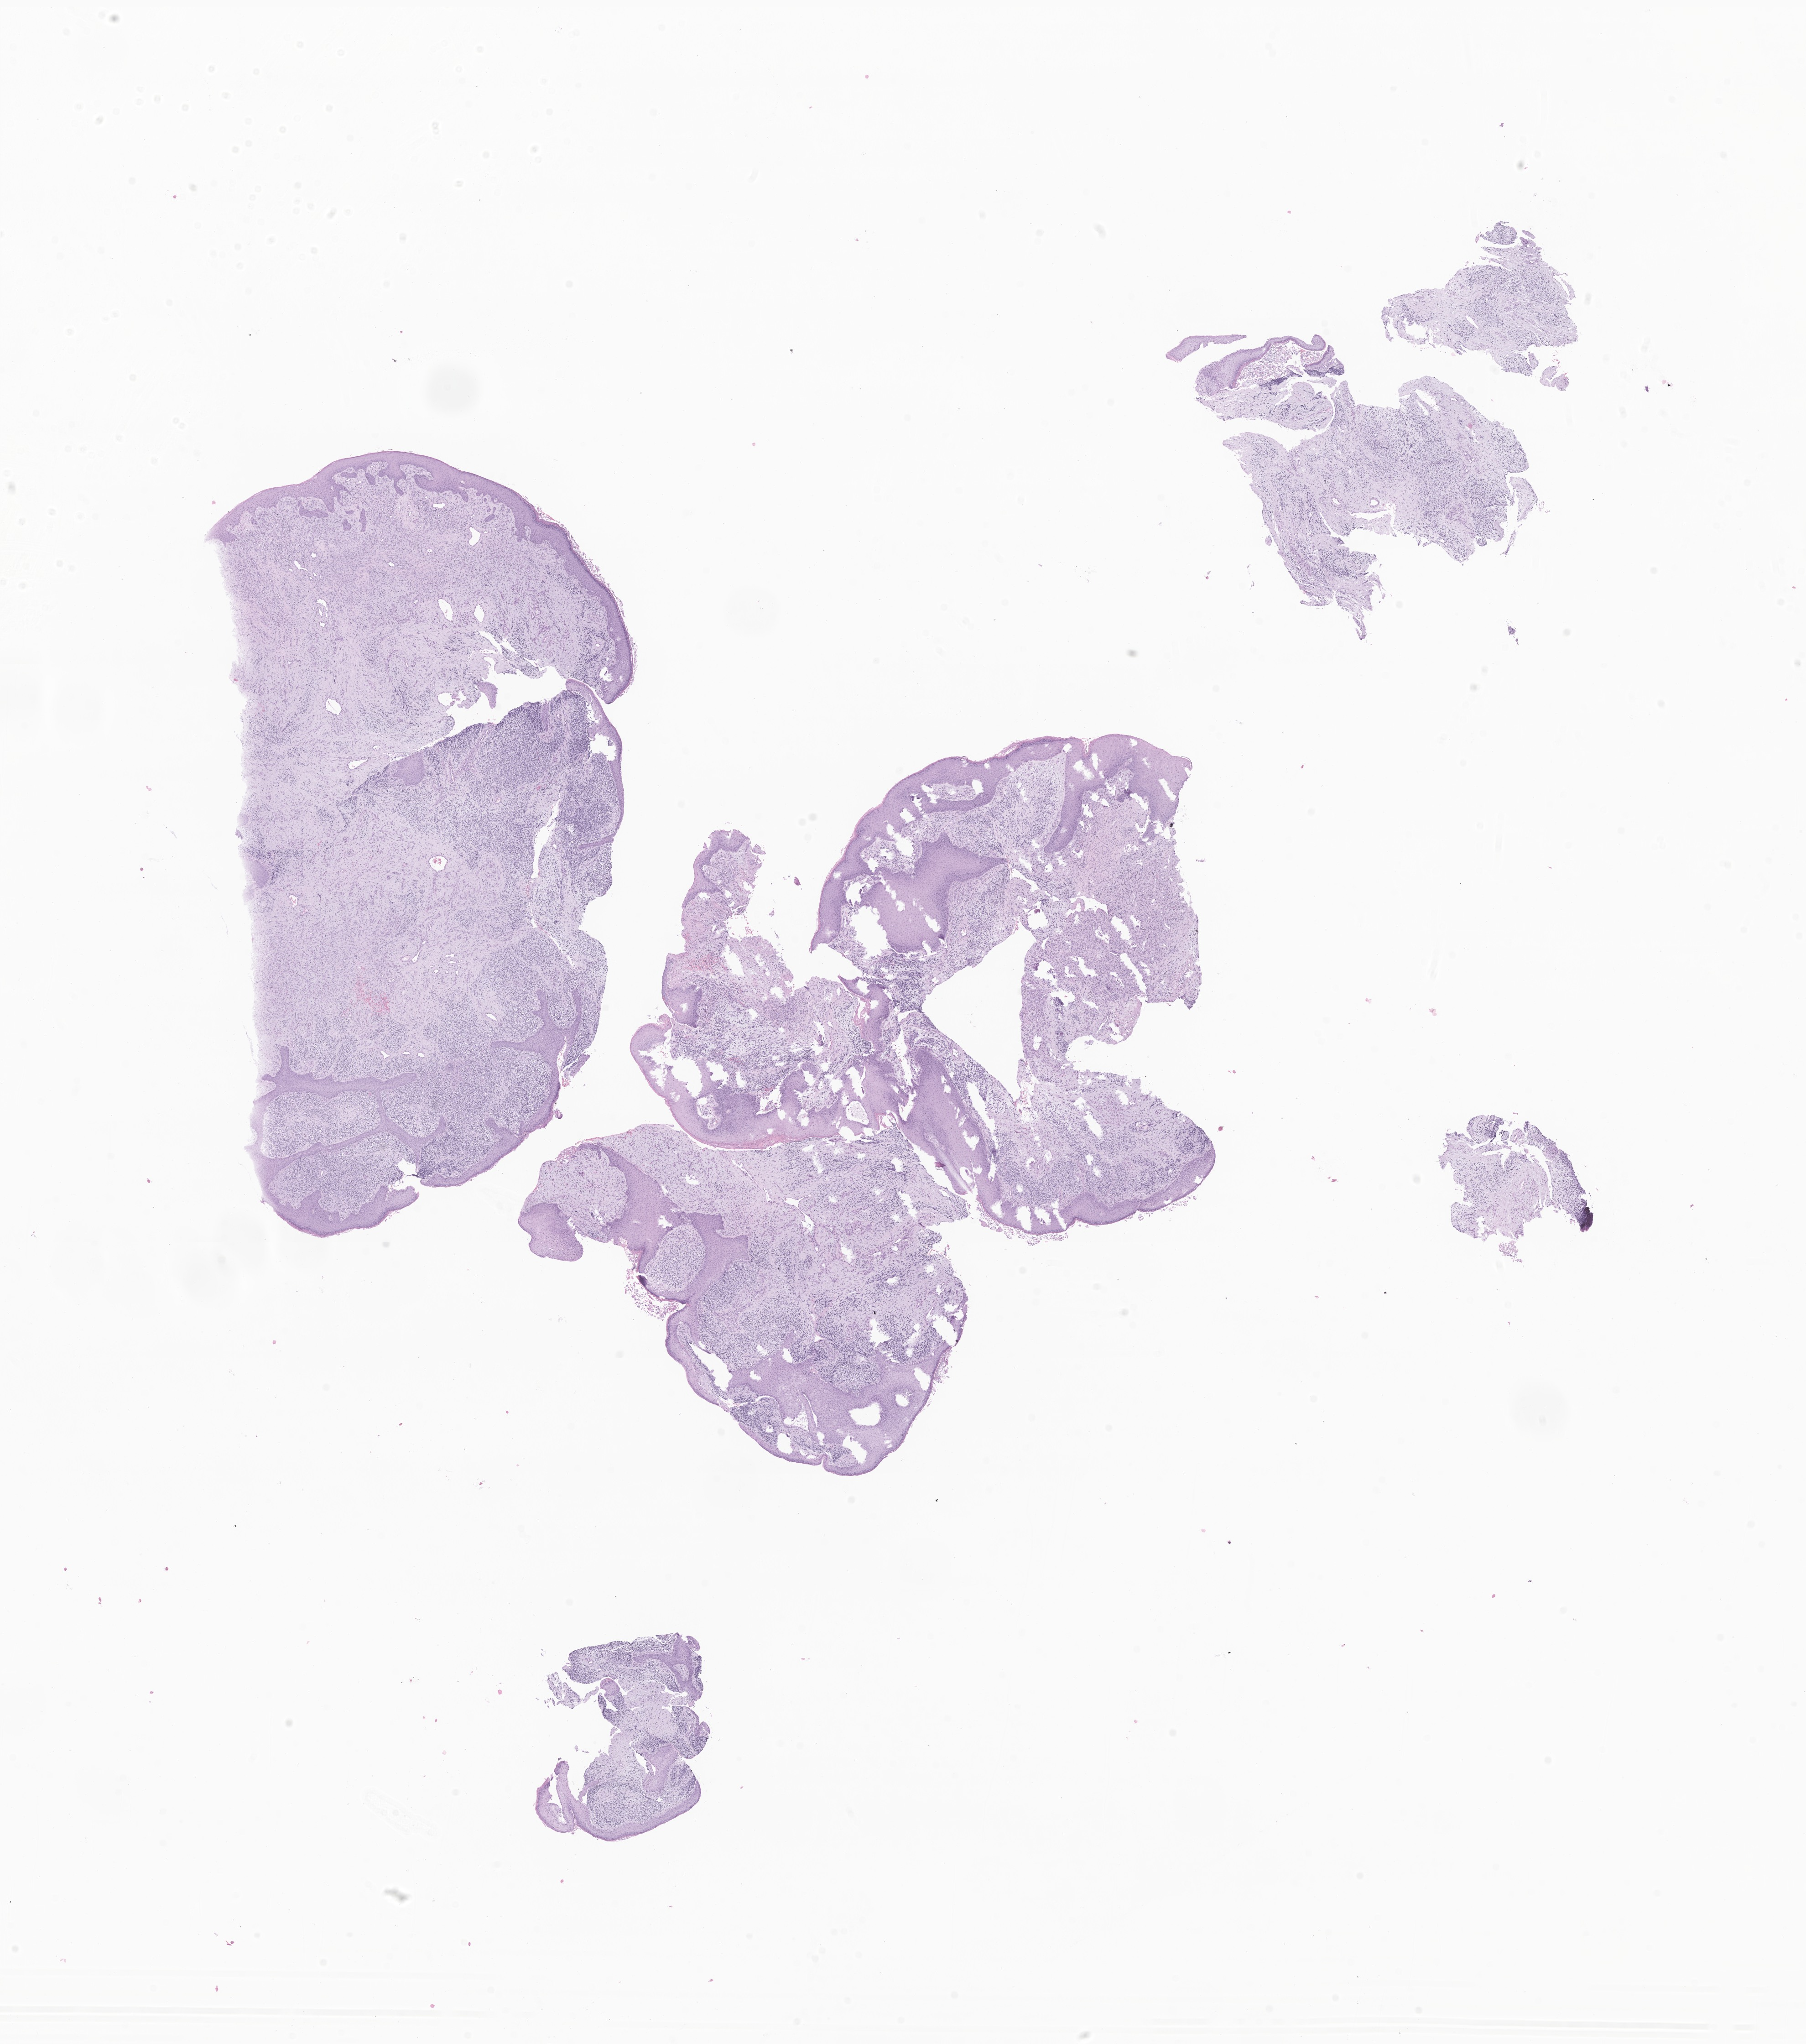
Digitized hematoxylin and eosin (H&E)-stained section of tumor tissue from the middle ear, whole scanned area (about 16.7 x 18.9 mm) shown as a low-resolution overview, formalin-fixed paraffin-embedded section. Patient male; age 66 months (5 years 6 months).
Recorded diagnosis: Rhabdomyosarcoma, NOS.